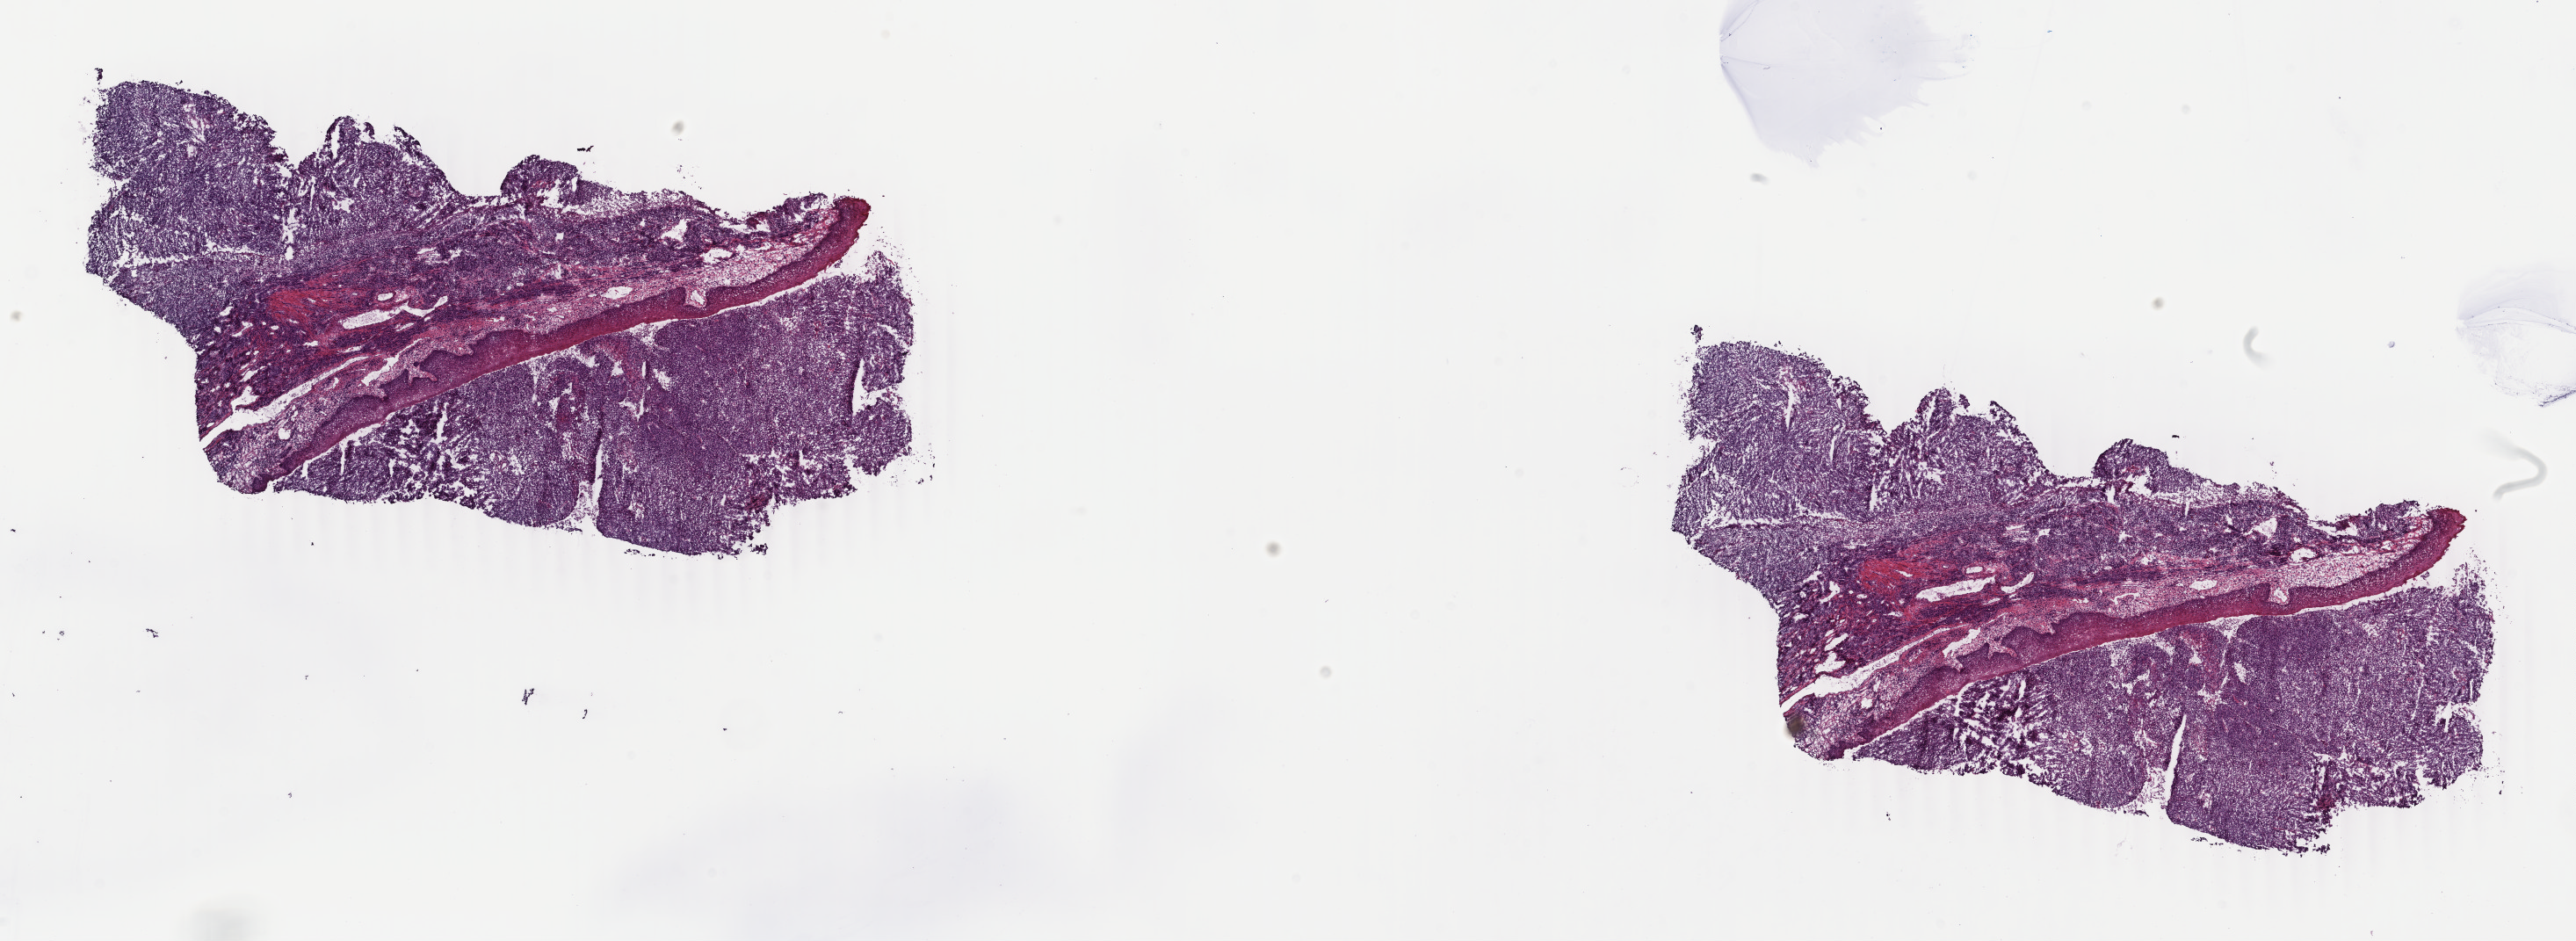
Whole-slide histology image, Hematoxylin and eosin (H&E) stained, low-resolution overview of the scanned area, about 23.3 x 8.5 mm (slide scanned at 40x), frozen section, head and neck, primary tumour sample. Patient: male, age at initial diagnosis 53 years. Pathologist review of this section (percent, as recorded): tumour cells 70%, tumour nuclei 80%, normal cells 10%, stromal cells 20%, necrosis 0%. Inflammatory infiltration, as recorded: lymphocyte infiltration 0%, monocyte infiltration 0%, neutrophil infiltration 0%.
Pathologic diagnosis: Squamous cell carcinoma, NOS.